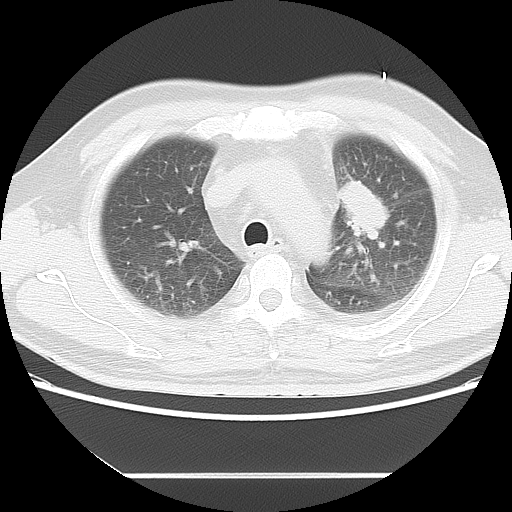
Chest CT, one axial slice; reconstruction kernel LUNG; 120 kVp; lung window (W 1500 / L -600 HU); 512 × 512 image matrix, field of view 350 × 350 mm. Patient: male, 56 years. From the clinical record (not read from this slice): clinical TNM (as recorded): T2 N3 M1.
Structures marked on this image (rectangle marked by the reading radiologist):
- lung tumour (recorded histology: adenocarcinoma): bounding box [x1, y1, x2, y2] px = [333, 169, 392, 245]